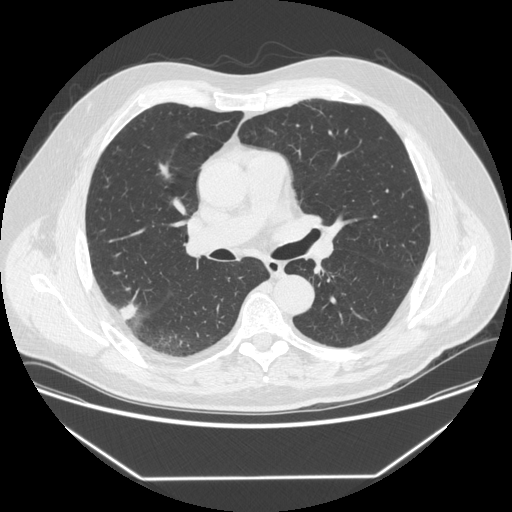
Low-dose screening chest CT, one axial slice; position 210 of 342 along the scan axis; lung window (W 1500 / L -600 HU); 1.25 mm slice thickness; 512 × 512 image matrix, field of view 410 × 410 mm.
Outlined on this slice (manually delineated by an expert):
- lesion 1 (tumor, upper lobe of right lung): bounding box <120,302,138,321> (left, top, right, bottom; pixels)